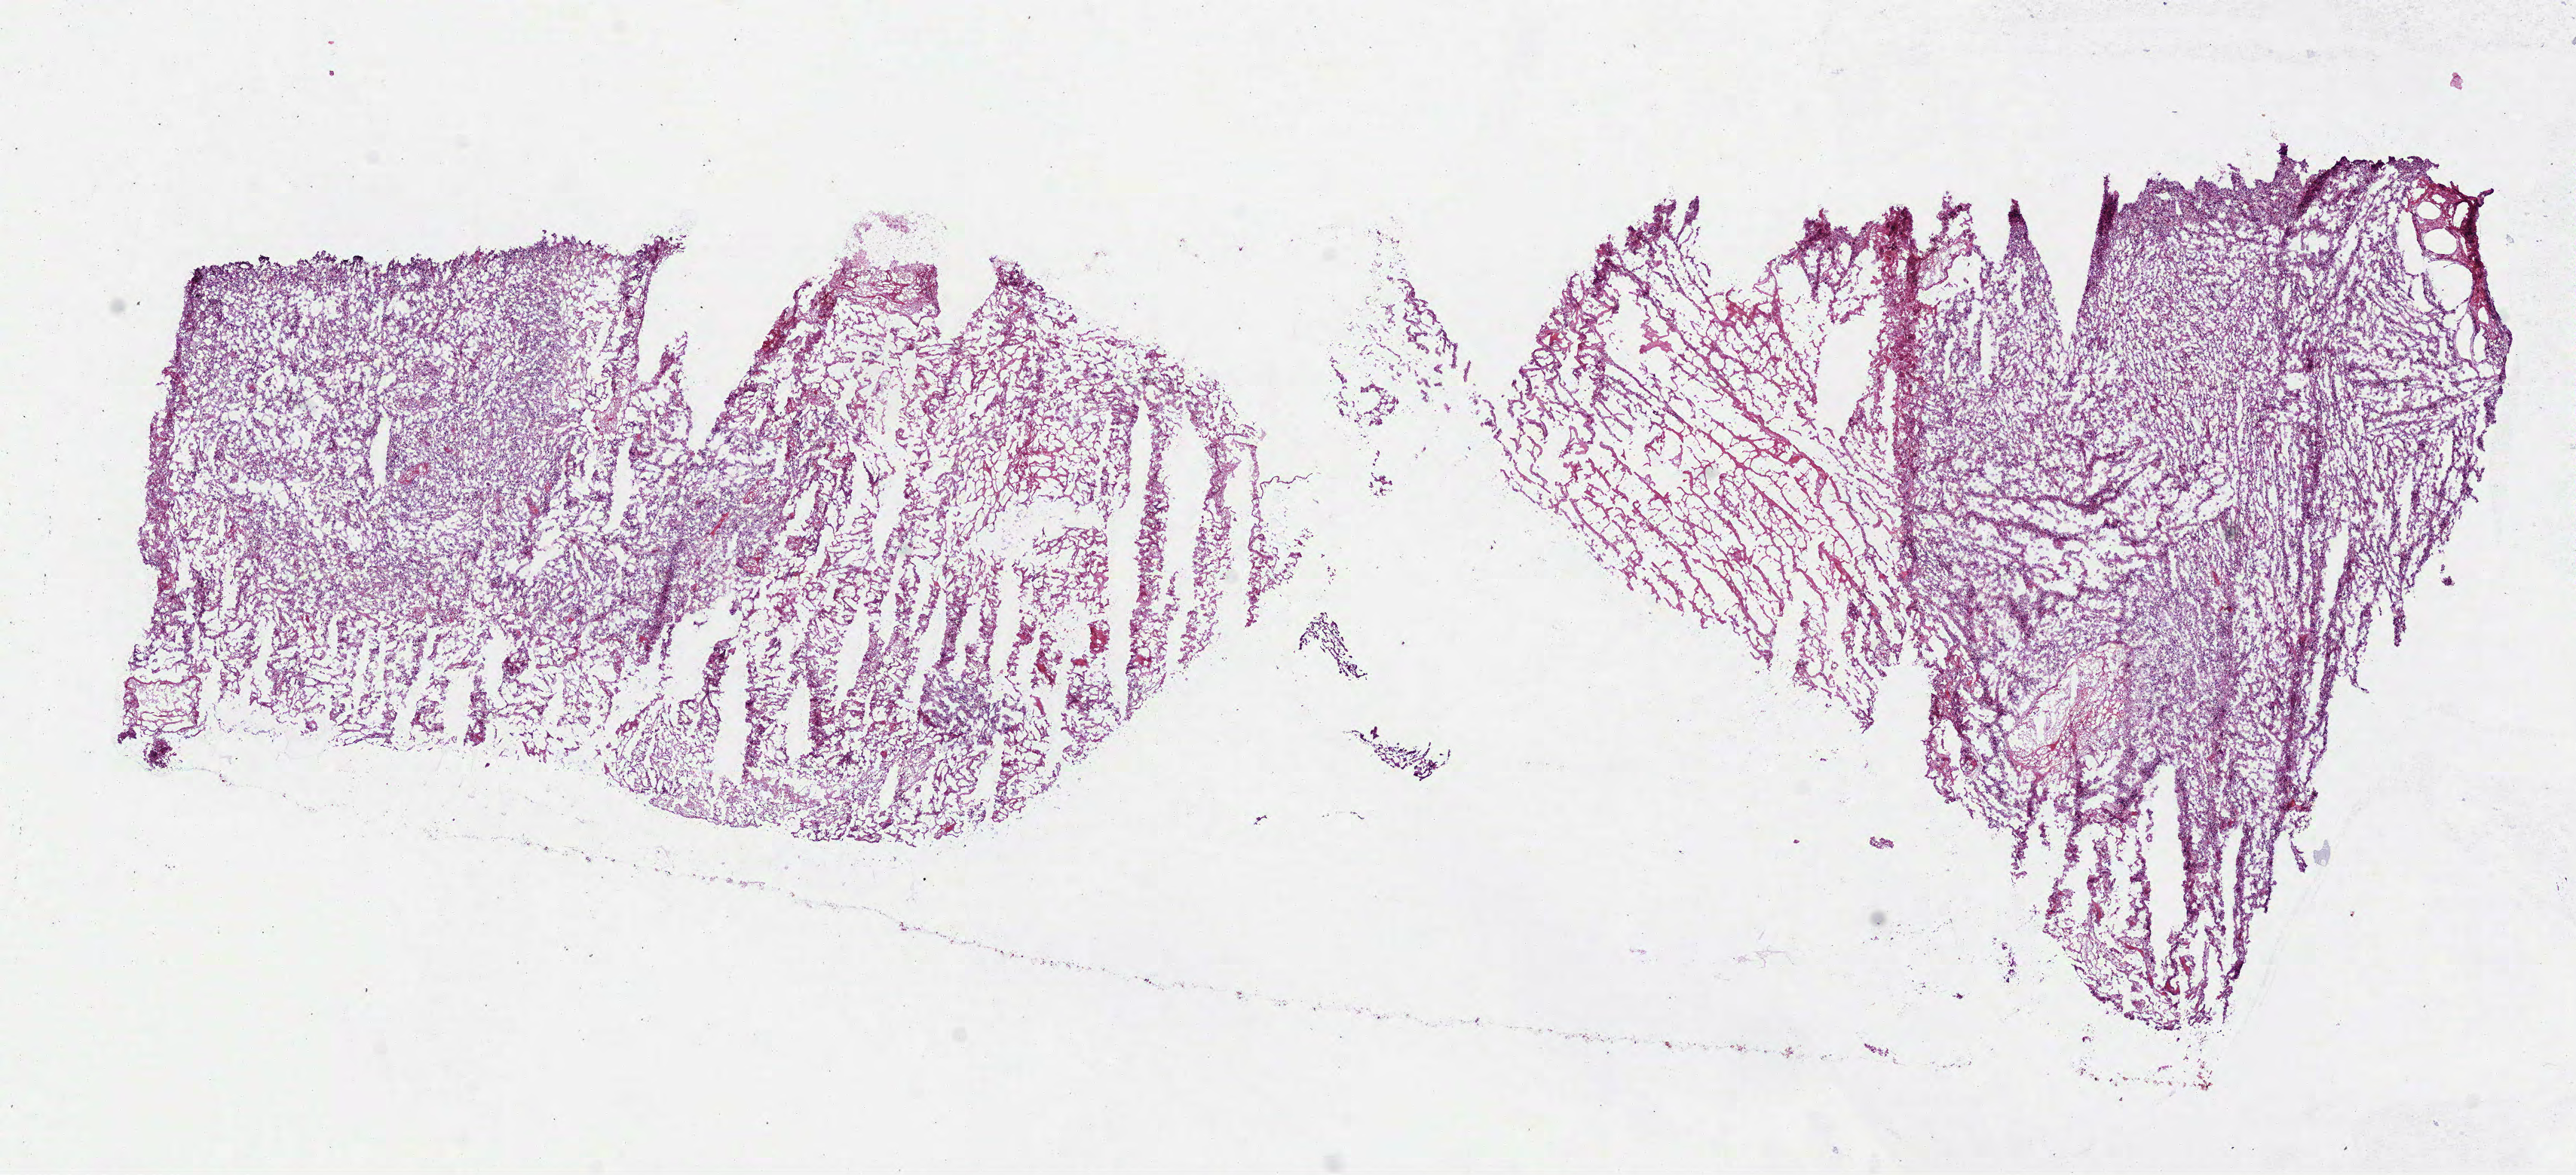
Whole-slide histology image, Hematoxylin and eosin (H&E) stained, whole scanned area (about 13.8 x 6.3 mm) shown as a low-resolution overview; frozen section; primary tumour sample from the brain. Male, age 57 years at initial diagnosis. Composition of this section per pathologist review: tumour cells 70%, tumour nuclei 75%.
Histologic diagnosis: Glioblastoma.